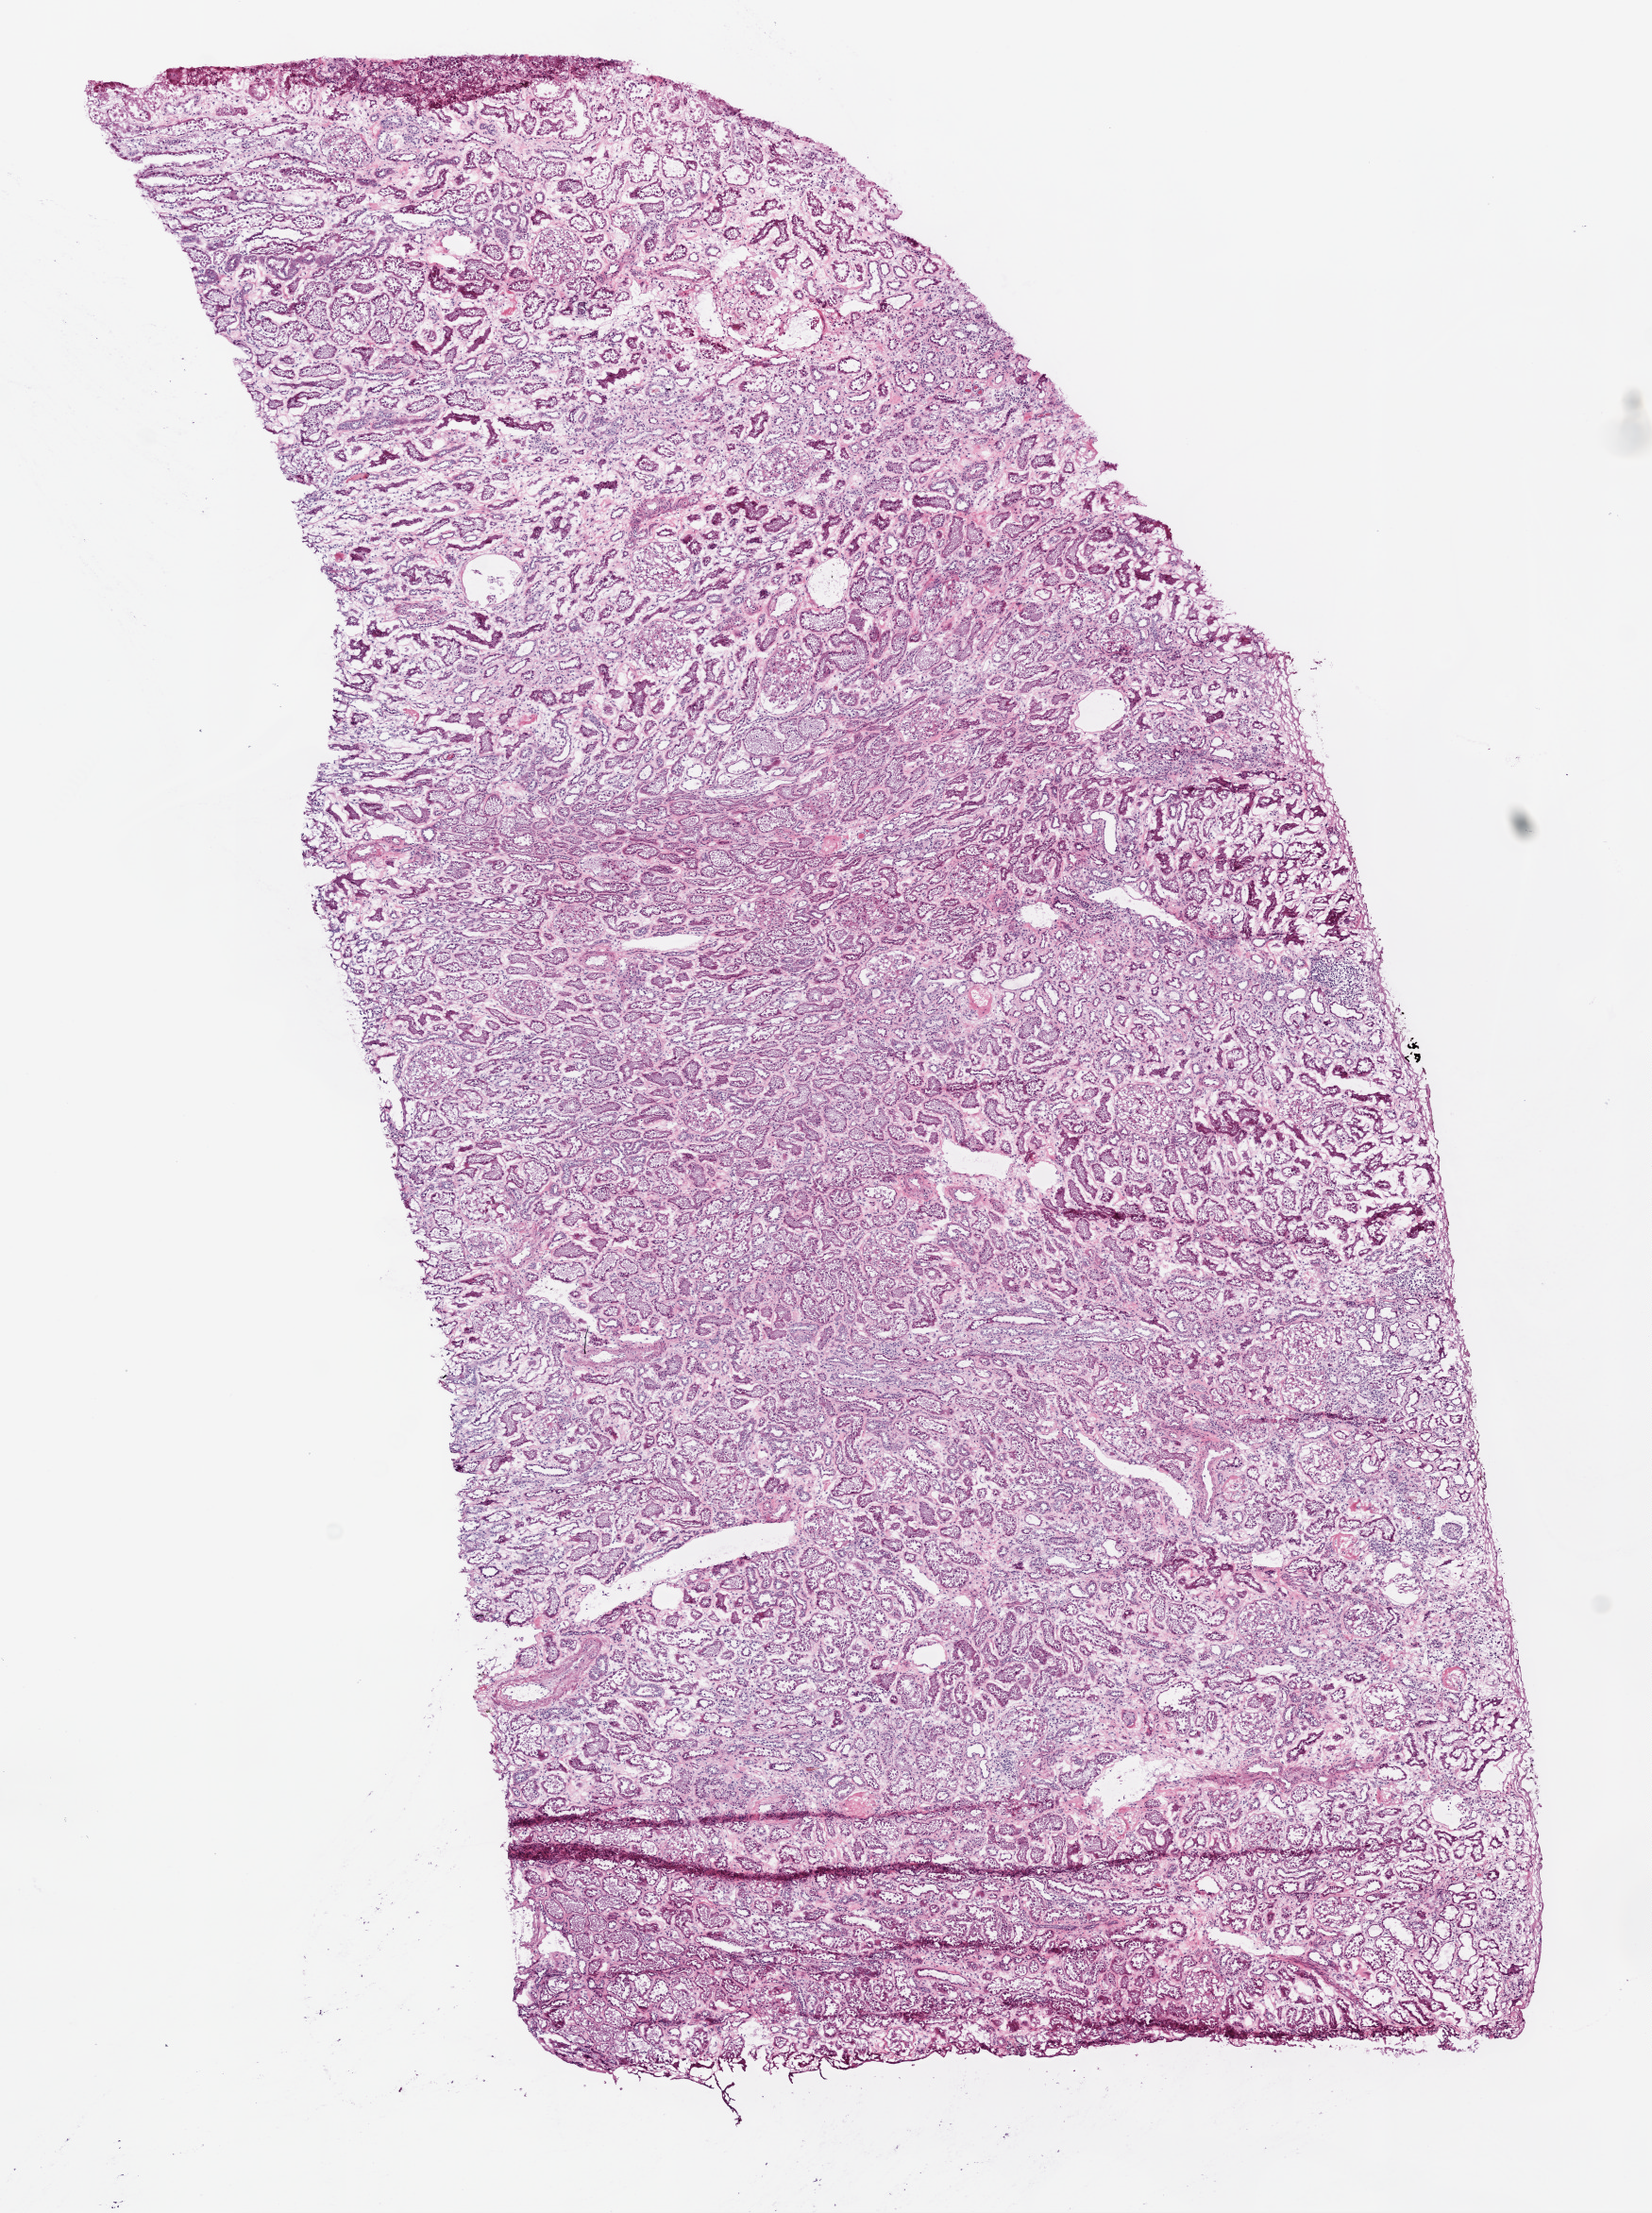
Digitized H&E-stained tissue section (whole slide) — whole scanned area (about 7.0 x 9.4 mm, acquisition: 20x scan) shown as a low-resolution overview, frozen section from the bottom of the tissue portion, sample: solid tissue normal (non-tumour tissue), kidney. Male patient; age at initial diagnosis 52 years.
This section: solid tissue normal (non-tumour) sample from the same patient. Patient diagnosis: Papillary adenocarcinoma, NOS.